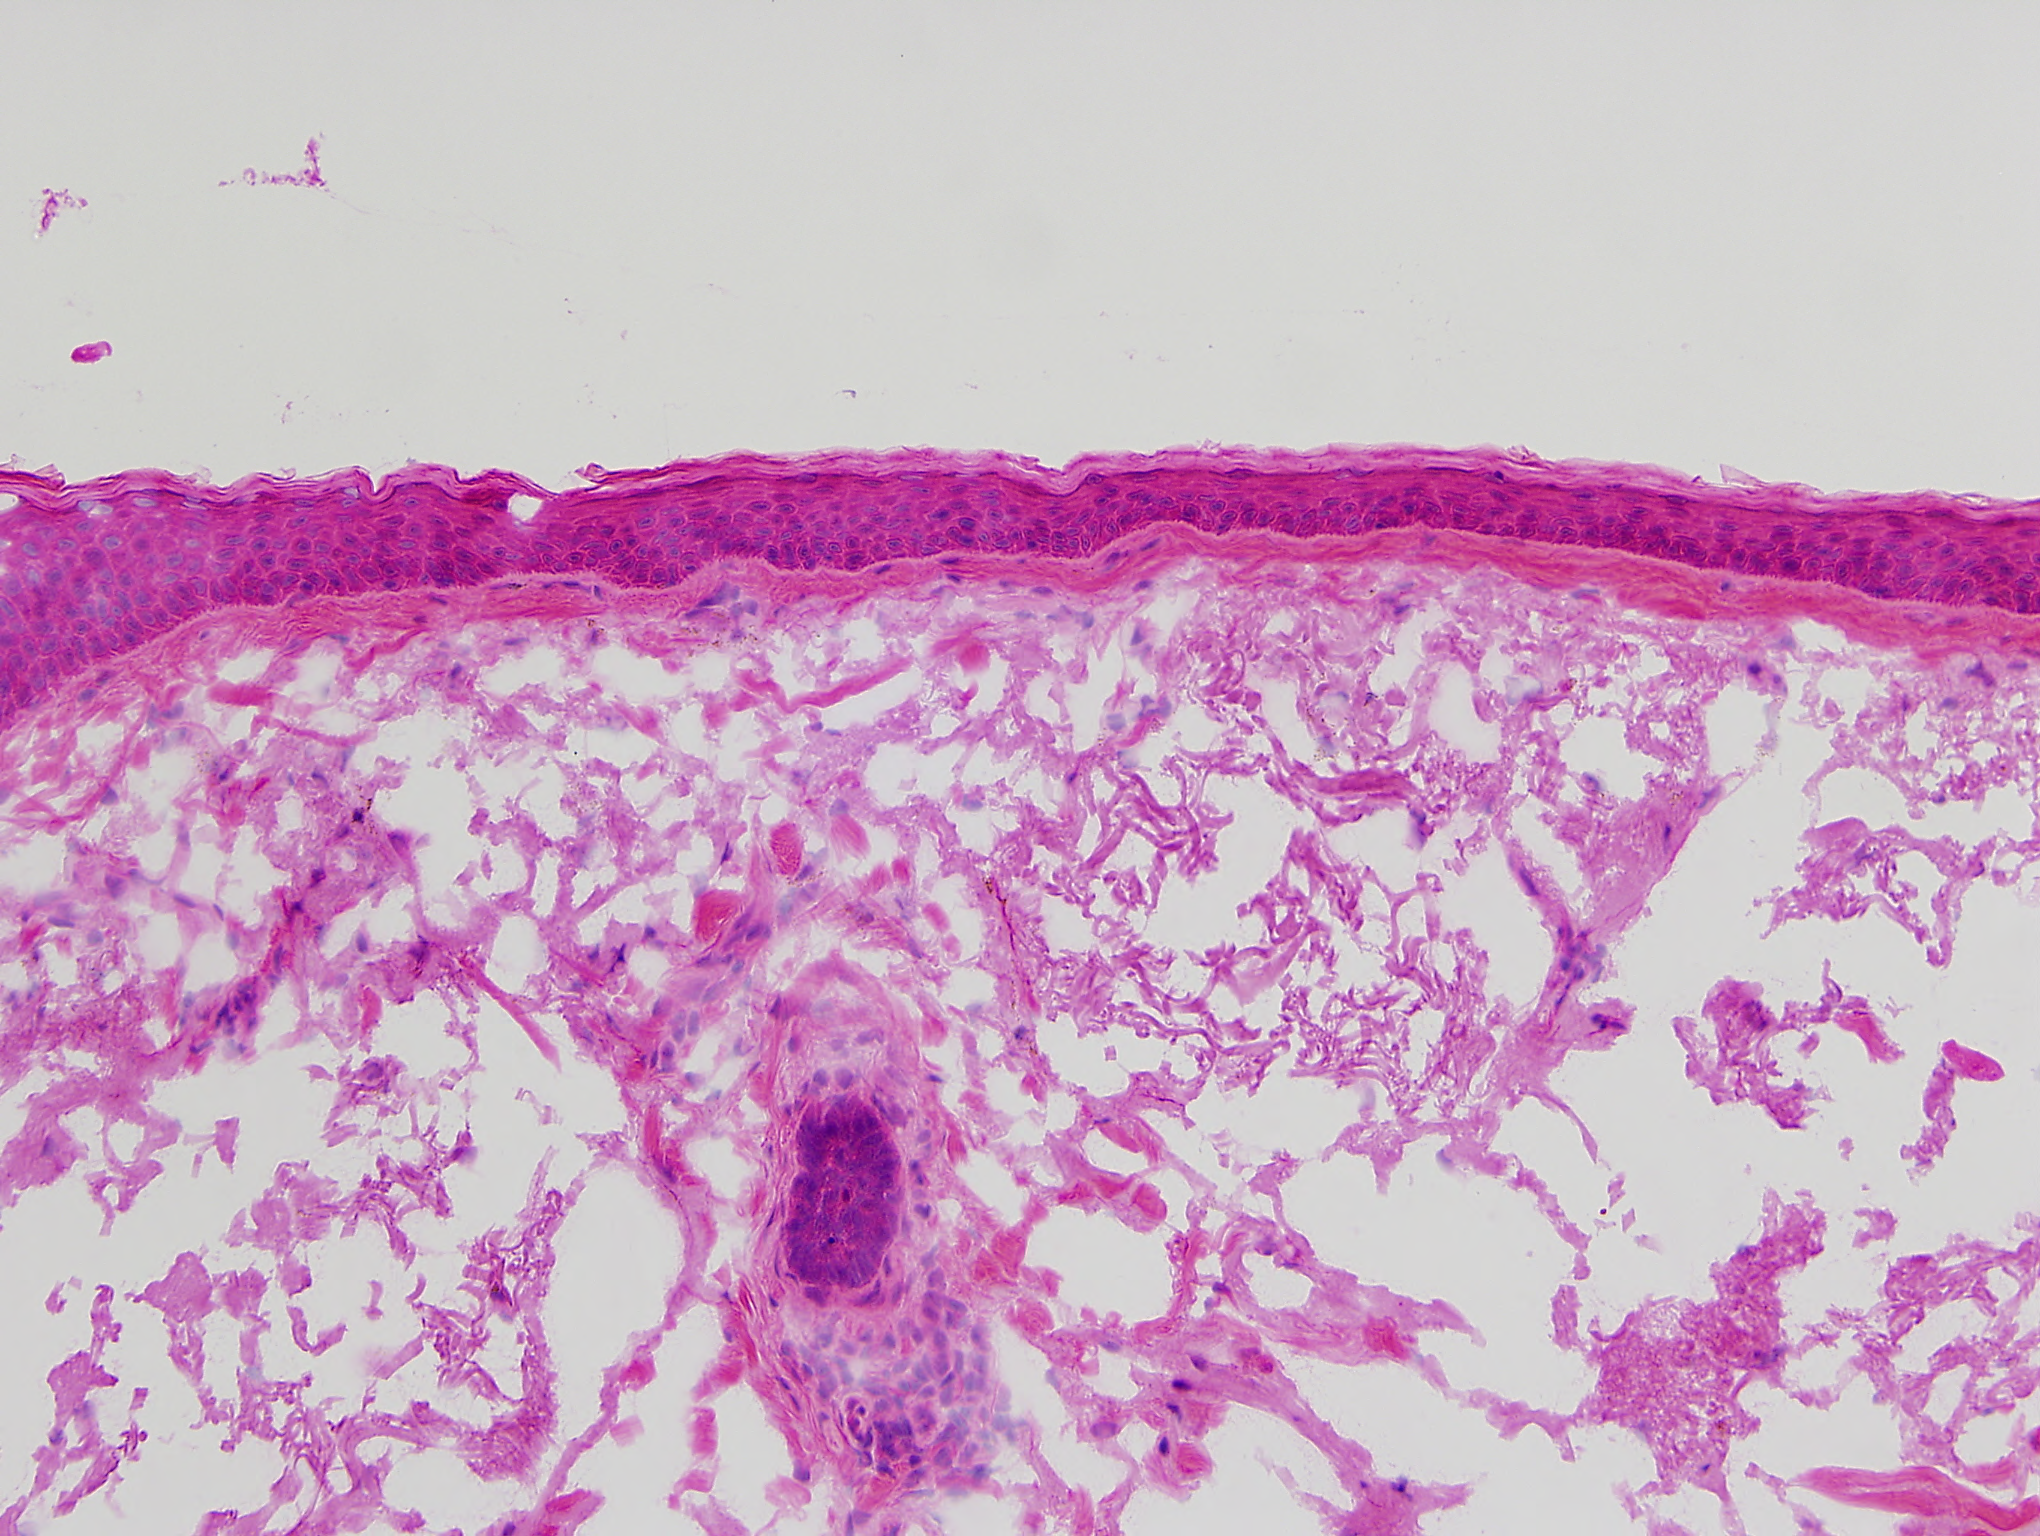
Hematoxylin and eosin (H&E) stained image of one small field of the section, roughly 1.0 x 0.8 mm in extent; frozen section from the top of the tissue portion; sample: solid tissue normal (non-tumour tissue), head and neck. Female patient; age at initial diagnosis 74 years. Inflammatory infiltration, as recorded: lymphocyte infiltration 0%, monocyte infiltration 0%, neutrophil infiltration 0%.
This section: solid tissue normal sample (biorepository sample class). Patient diagnosis: Squamous cell carcinoma, NOS (overlapping lesion of lip, oral cavity and pharynx).